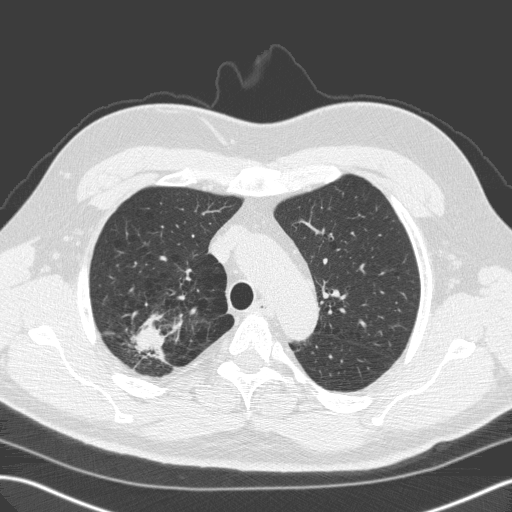
Chest CT (low-dose screening protocol), one axial image, first (baseline) screen, lung window (W 1500 / L -600 HU), standard (soft-tissue) reconstruction kernel (C), 512 × 512 image matrix, field of view 357 × 357 mm. Male, age 59 years at enrolment. Former smoker at enrolment.
Expert reader's lesion annotation, bounding box (x1, y1, x2, y2) in pixels: (117, 309, 178, 372). Reader record for this screening exam (exam-level; its link to the box is not recorded): non-calcified nodule or mass ≥4 mm, right upper lobe, 28 × 25 mm, spiculated (stellate) margins, soft tissue attenuation. Later outcome: lung cancer diagnosed 64 days after this screen — large cell carcinoma, NOS, right upper lobe, undifferentiated (G4), stage IA (AJCC 6th edition), 25 mm at pathology.